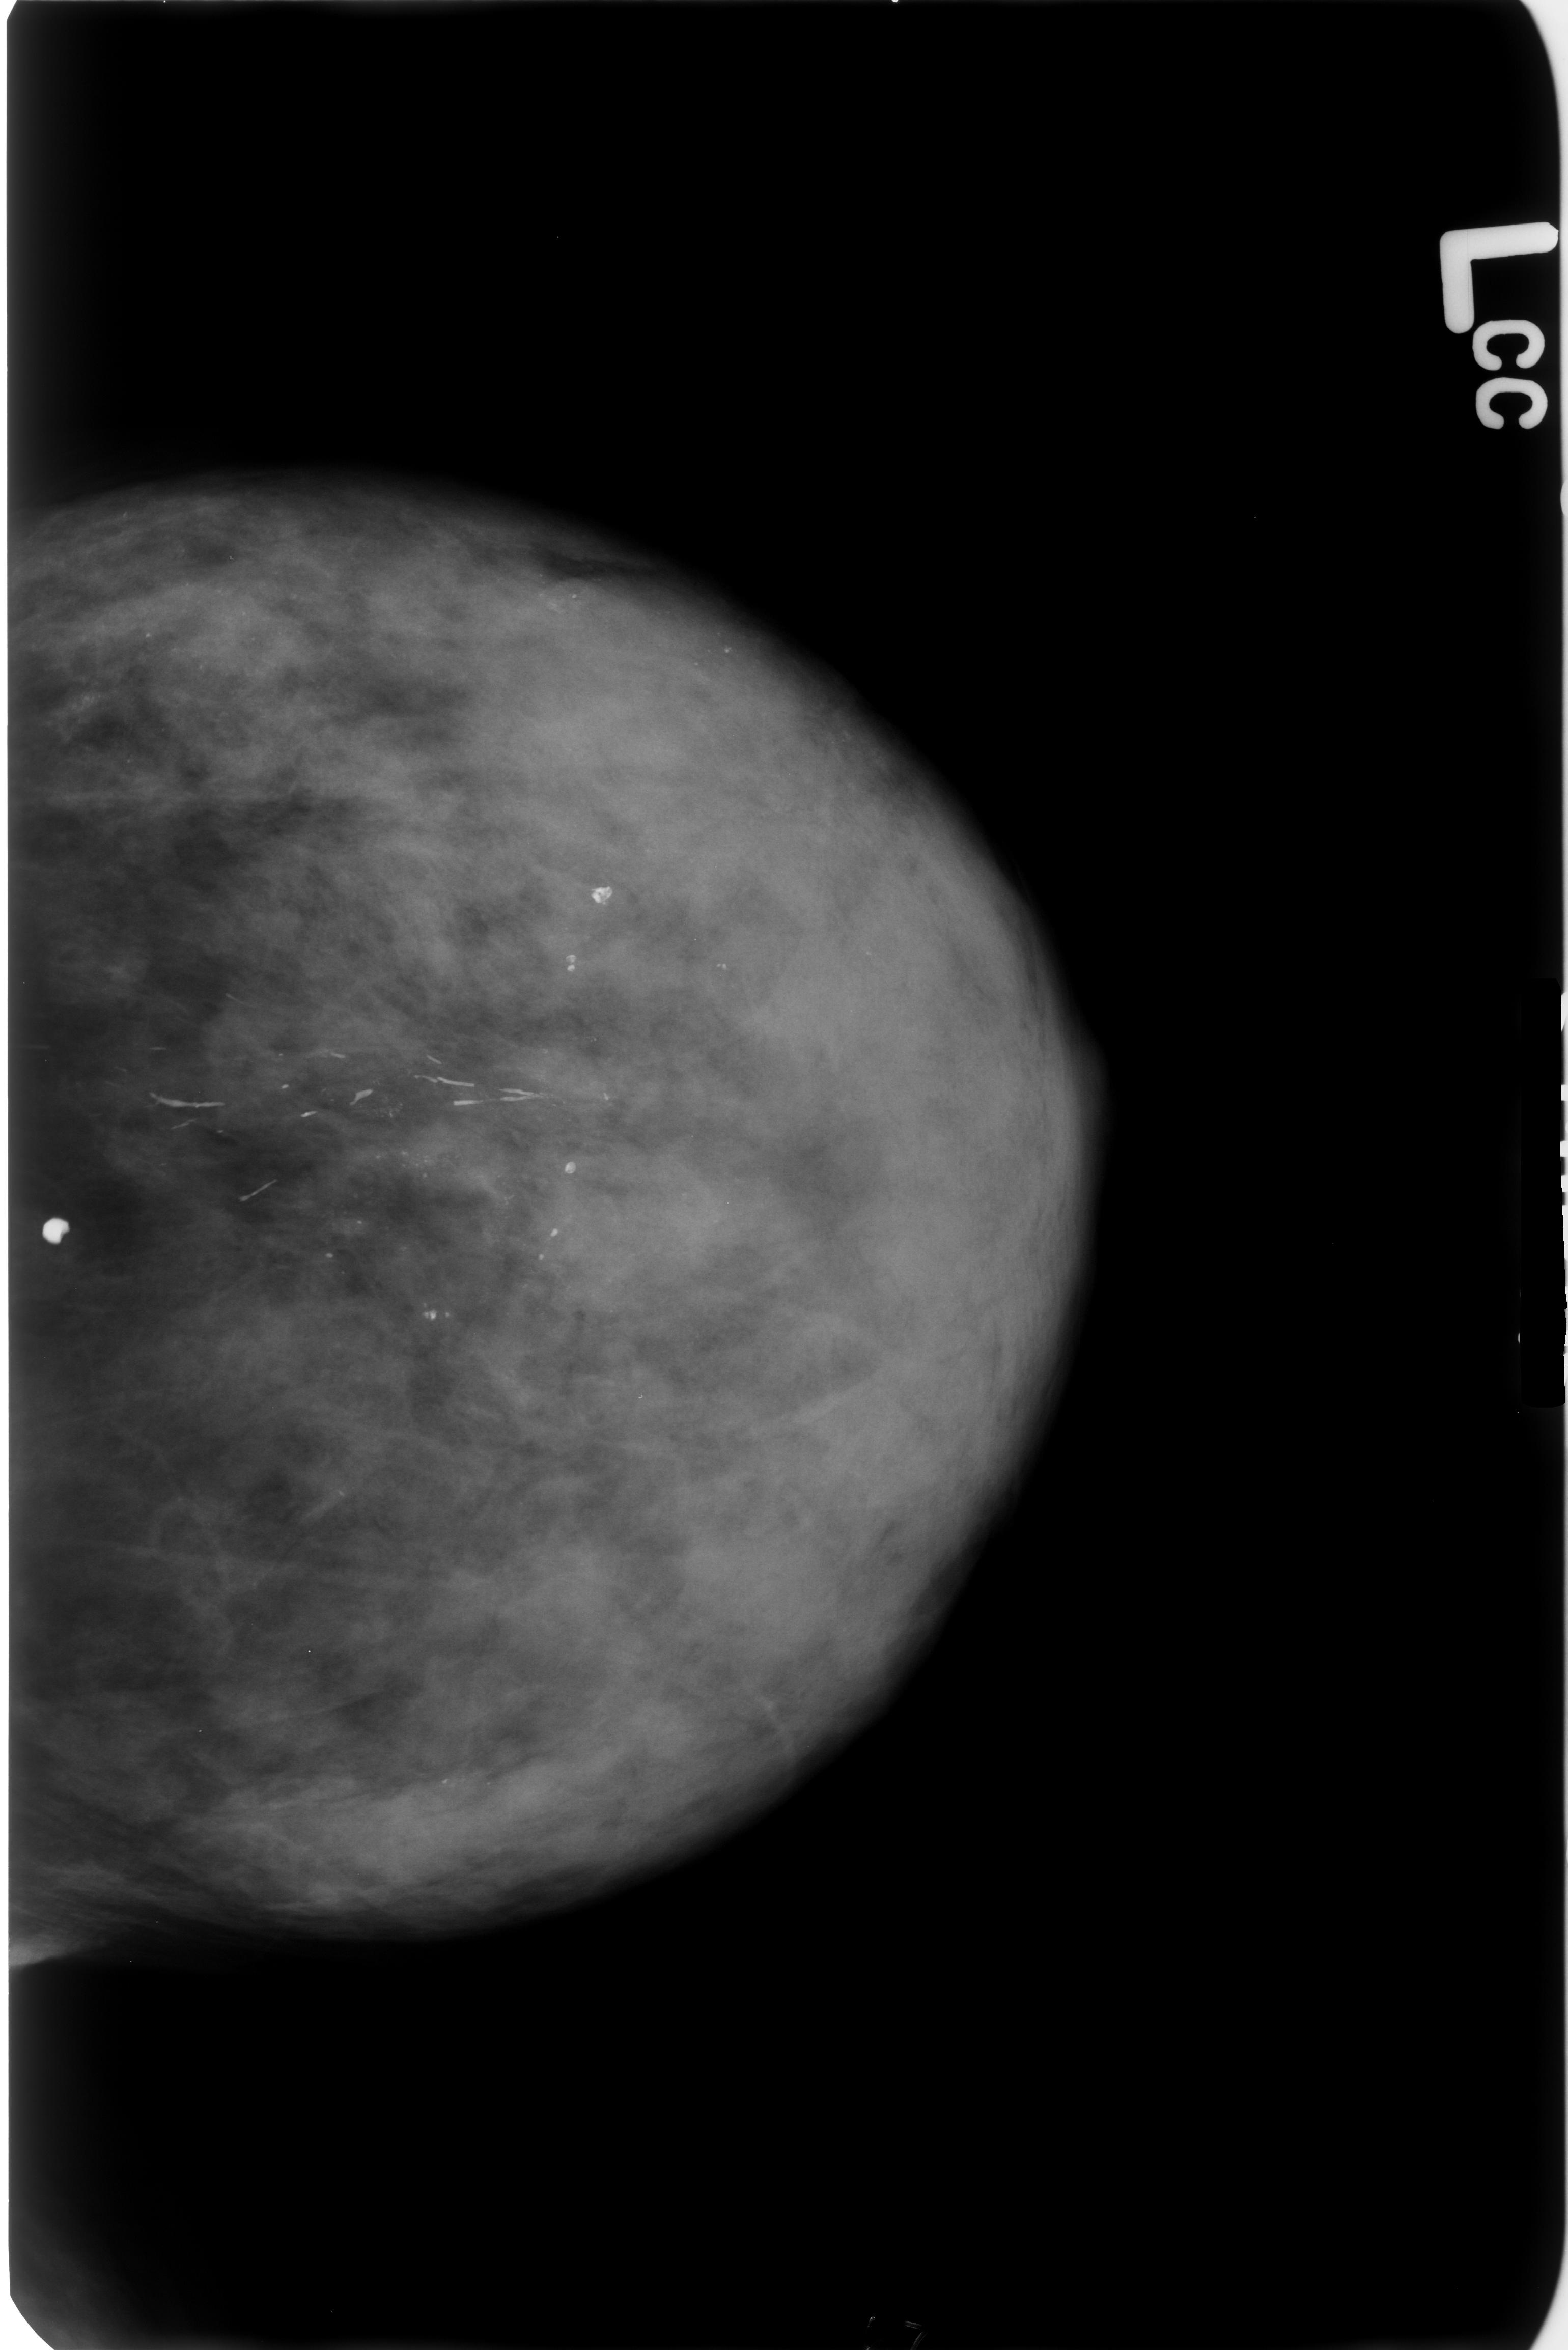
Digitized screen-film mammogram. Left breast. CC view. BI-RADS breast density category 4 (scale 1–4). 1568 × 2350 image matrix.
Expert-marked regions of interest on this film, with their recorded descriptors:
- calcifications, morphology punctate / lucent center, distribution regional; BI-RADS assessment category 2; benign; no additional work-up was recommended (outcome (as recorded, no biopsy): benign without callback): bounding box [x1, y1, x2, y2] px = [134, 1034, 555, 1219]